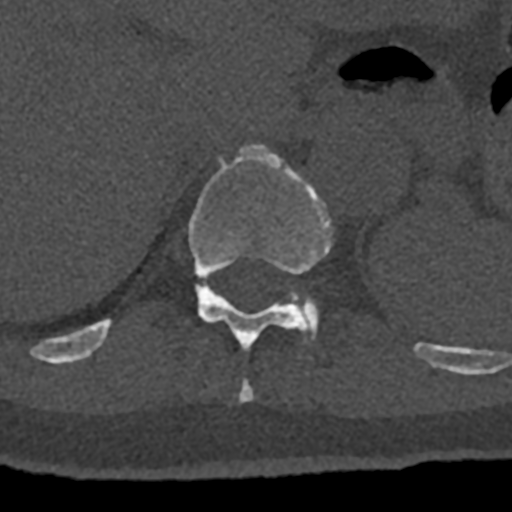
CT including the spine, one axial slice; slice 543 of 797 in the series (ordered by position); reconstruction kernel Br40s/3; bone window (W 1800 / L 400 HU); 512 × 512 image matrix, field of view 160 × 160 mm. Patient: male, 74 years. Case-level facts recorded for this patient, not image findings: primary cancer: renal; vertebrae with lytic lesions (as recorded): T10, L1, L2, L3, L4, L5.
Annotated regions visible in this slice (semi-automatic segmentation, software-assisted and operator-edited):
- T10 vertebra: box from (x=239, y=382) to (x=254, y=402) px
- T11 vertebra: (x=70, y=144)–(x=432, y=365)
- T12 vertebra: (x=290, y=291)–(x=319, y=339)